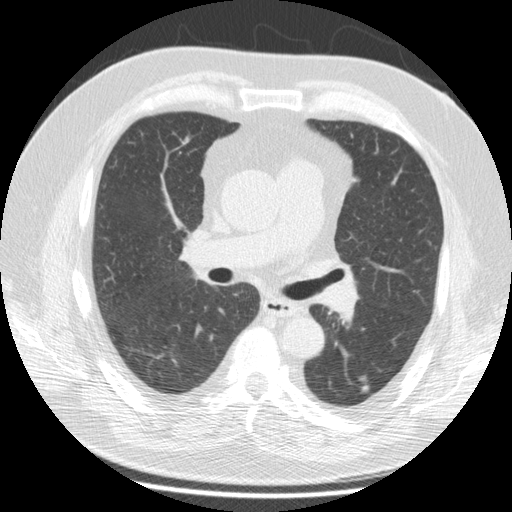
Axial slice from a low-dose chest CT screening exam, third screening round (two years after baseline), lung window (W 1500 / L -600 HU), 2.5 mm slice thickness, standard (soft-tissue) reconstruction kernel (STANDARD), 120 kVp. Male participant, aged 69 years at enrolment. Former smoker at enrolment.
Expert reader's lesion annotation, bounding box (x1, y1, x2, y2) in pixels: (354, 372, 381, 402). The screening reader recorded 2 non-calcified nodules or masses ≥4 mm on this exam; which of them this box marks is not recorded. Later outcome: lung cancer diagnosed 224 days after this screen — squamous cell carcinoma, NOS, left lower lobe, moderately differentiated (G2), stage IA (AJCC 6th edition), 14 mm at pathology.